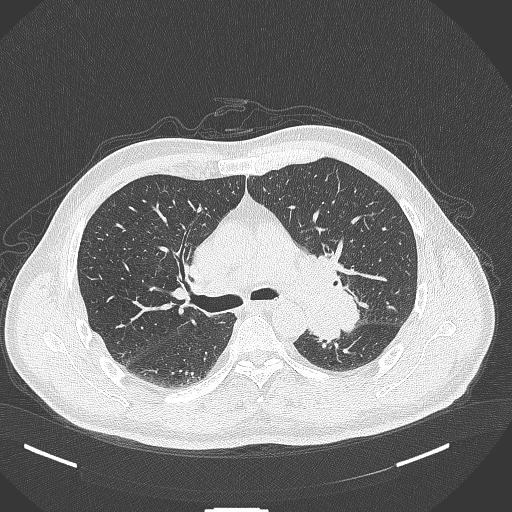
Chest CT, one axial slice. Slice 261 of 429 in the series (ordered by position). 120 kVp. Lung window (W 1500 / L -600 HU). 1 mm slice thickness. 512 × 512 image matrix, field of view 400 × 400 mm. Male patient, age 55 years. Case-level facts recorded for this patient, not image findings: clinical TNM (as recorded): T3 N0 M1c.
Annotated regions visible in this slice (bounding box drawn by a radiologist):
- lung tumour (recorded histology: adenocarcinoma): box from (x=295, y=278) to (x=362, y=341) px